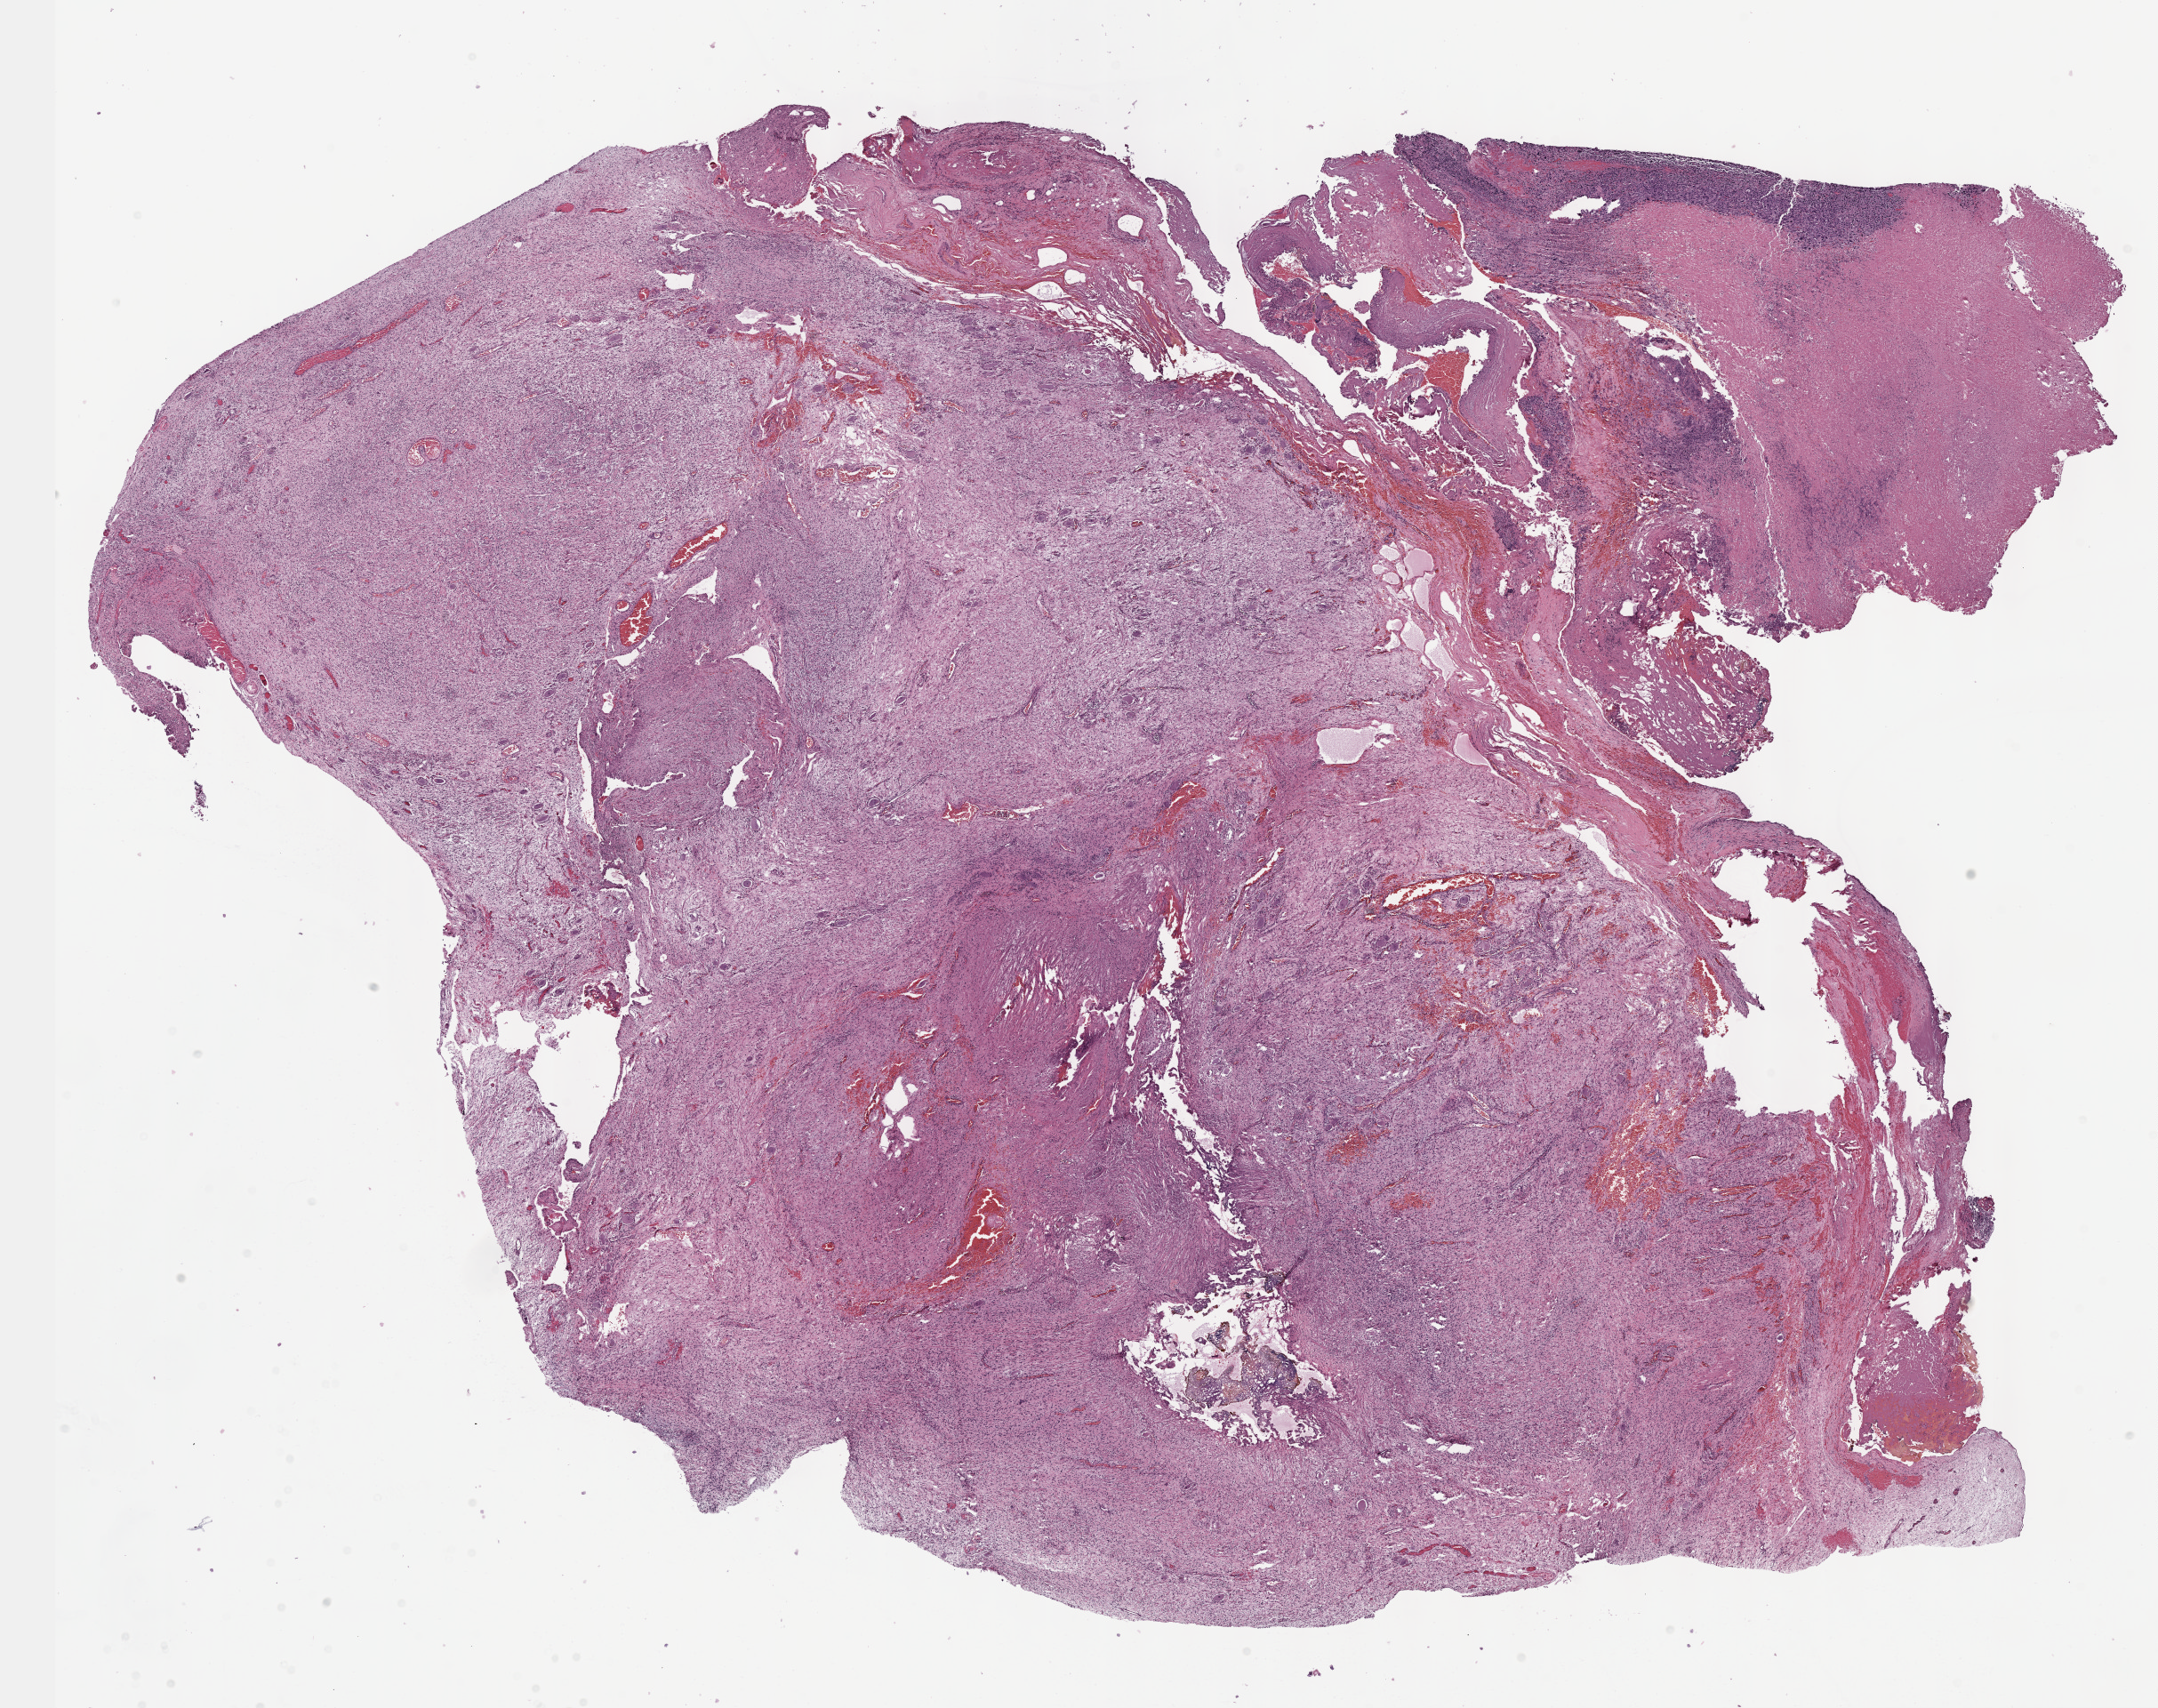
Whole-slide histology image, Hematoxylin and eosin (H&E) stained, shown as a low-resolution overview of the whole scanned area (about 19.6 x 15.5 mm, from a 40x scan), formalin-fixed paraffin-embedded (FFPE) diagnostic section, peripheral nerves and autonomic nervous system, primary tumour sample. Patient: male, age at initial diagnosis 50 years.
* diagnosis: Malignant peripheral nerve sheath tumor (peripheral nerves and autonomic nervous system of upper limb and shoulder)